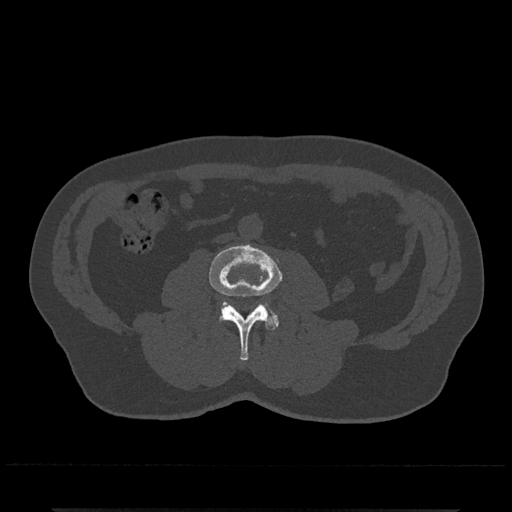
CT including the spine, one axial slice. Slice 208 of 797 in the series (ordered by position). Reconstruction kernel Br40s/3. Bone window (W 1800 / L 400 HU). 0.5 mm slice thickness. 512 × 512 image matrix, field of view 393 × 393 mm. Patient: male, 67 years. Case-level facts recorded for this patient, not image findings: primary cancer: prostate.
Outlined on this slice (semi-automatically segmented with operator editing):
- L3 vertebra: box from (x=209, y=244) to (x=282, y=361) px
- L4 vertebra: (x=221, y=301)–(x=279, y=327)